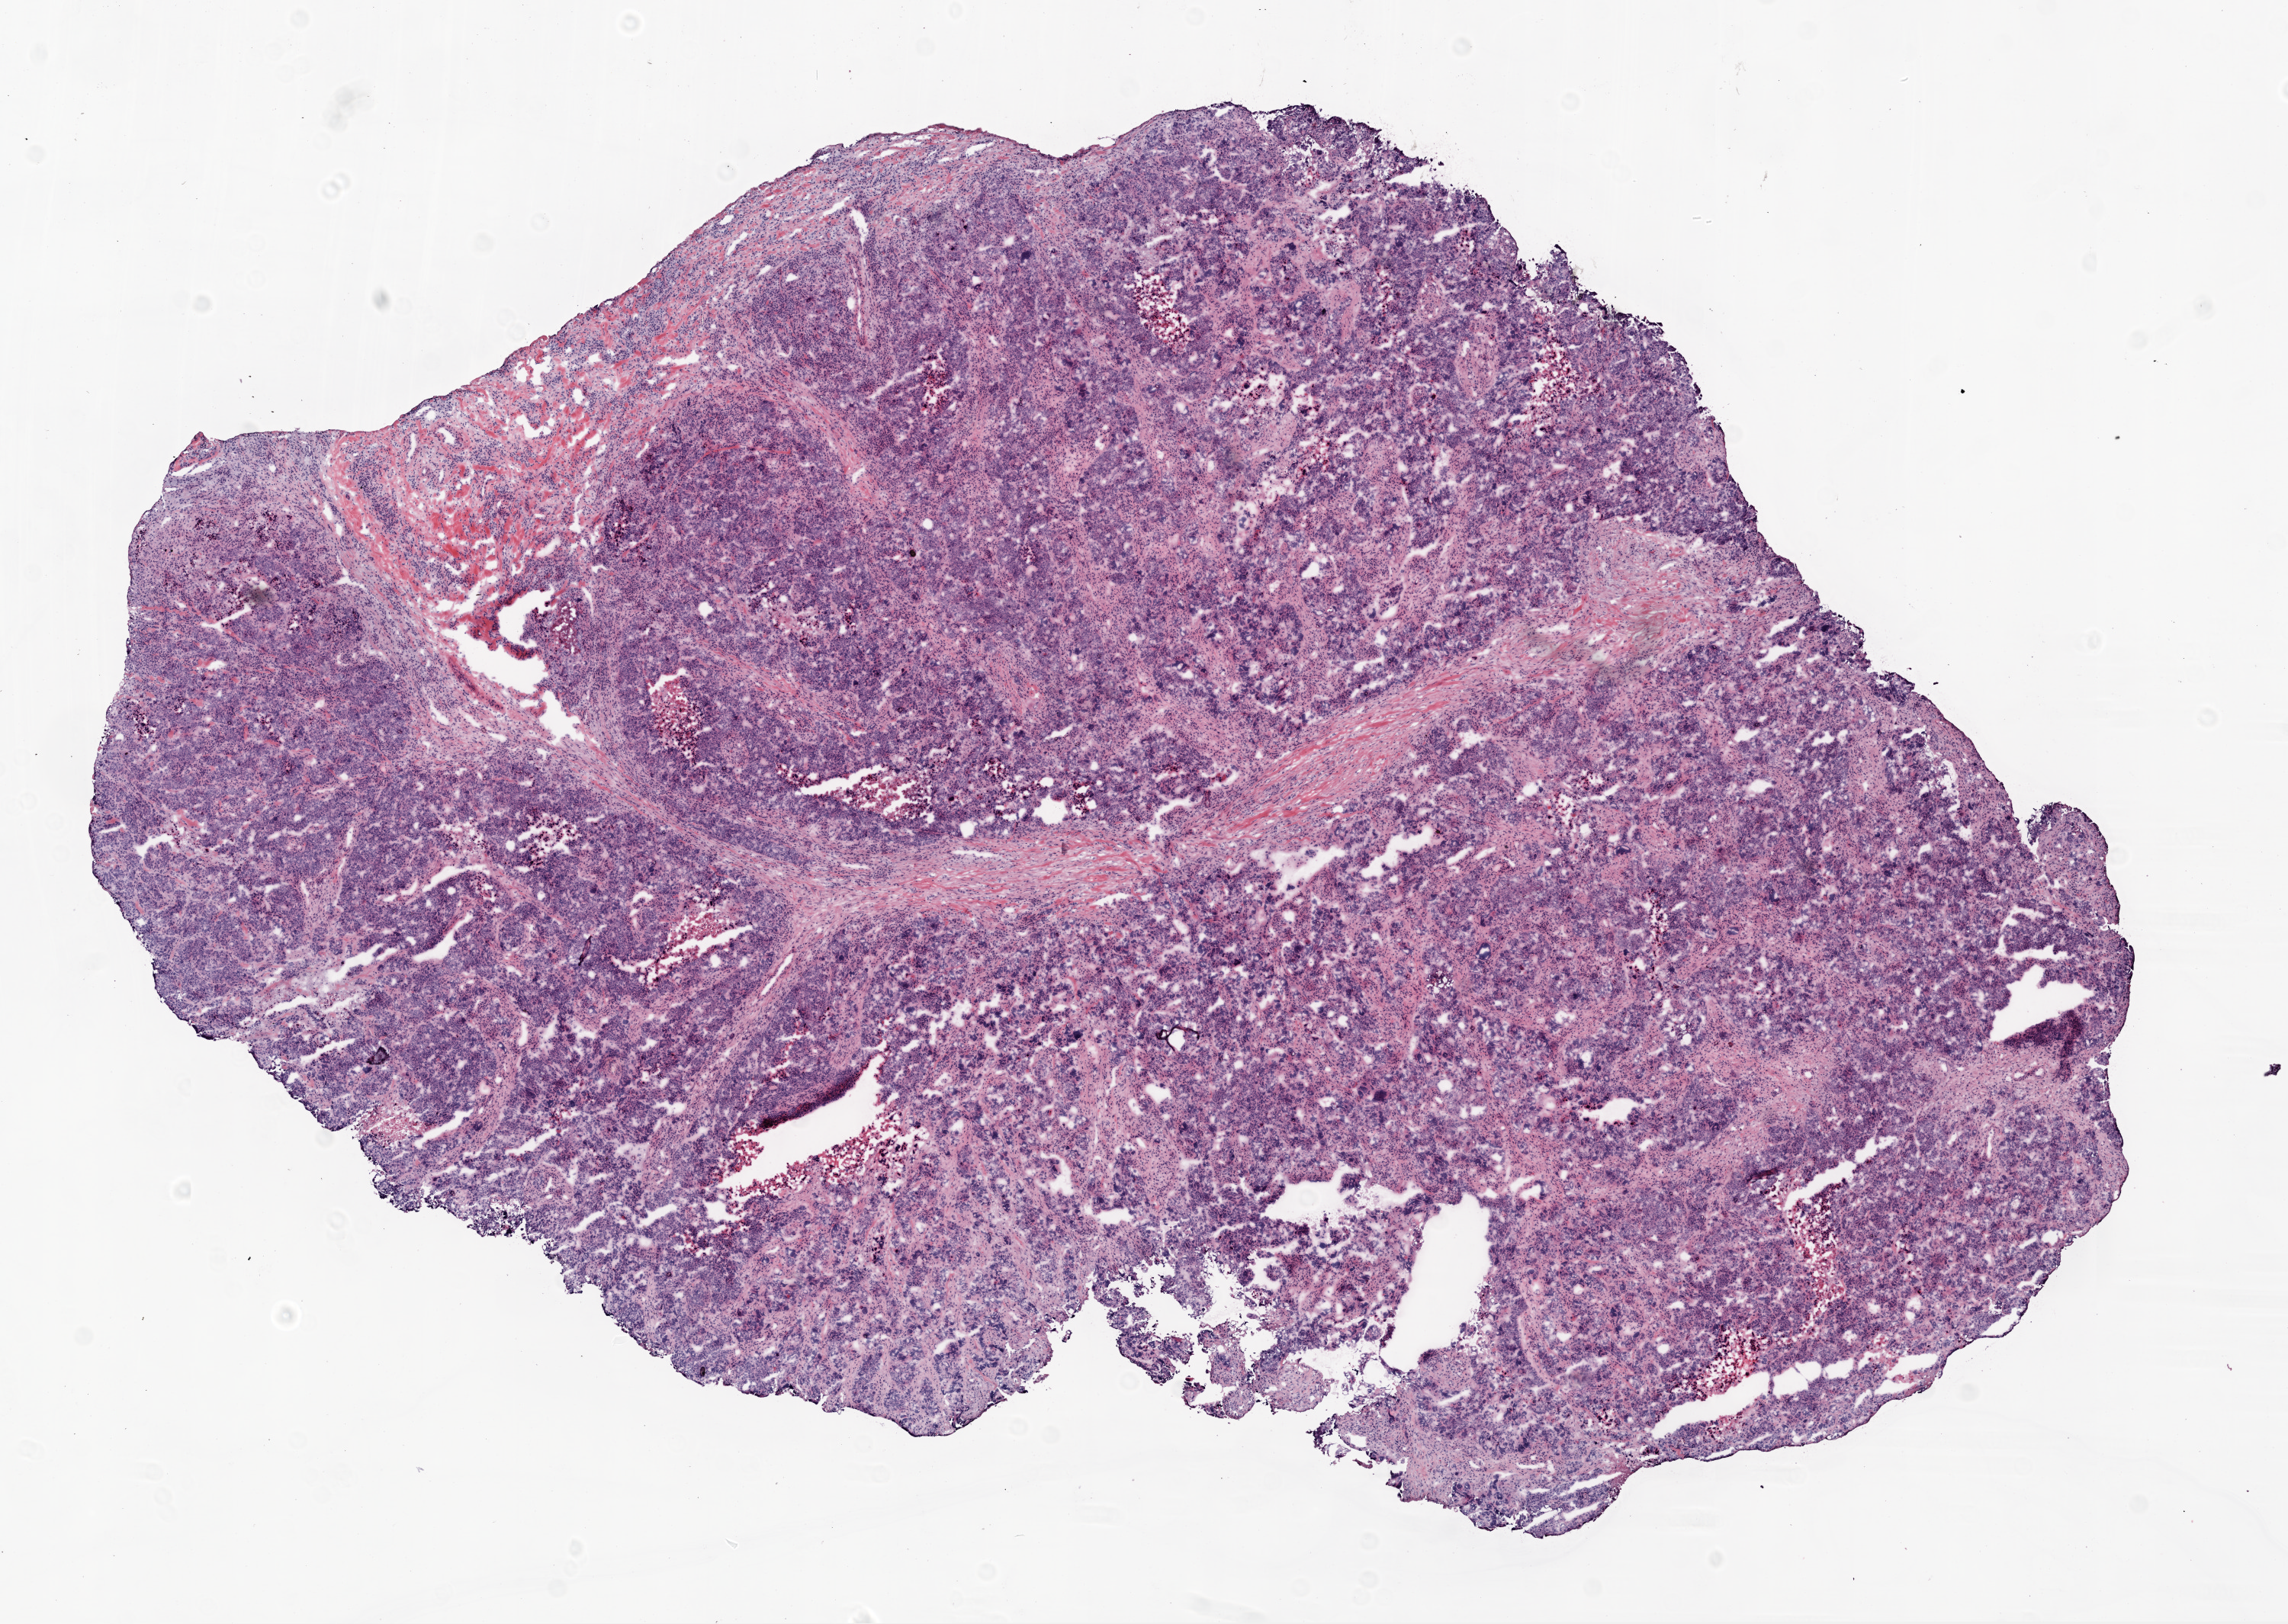
Whole-slide histology image, Hematoxylin and eosin (H&E) stained — low-resolution overview of the scanned area, about 12.0 x 8.5 mm, frozen section from the top of the tissue portion, ovary, recurrent tumour sample. Female patient; age at initial diagnosis 58 years. Pathologist review of this section (percent, as recorded): tumour cells 90%, tumour nuclei 95%, normal cells 0%, stromal cells 8%, necrosis 2%.
* this section: recurrent tumour
* patient diagnosis: Serous cystadenocarcinoma, NOS